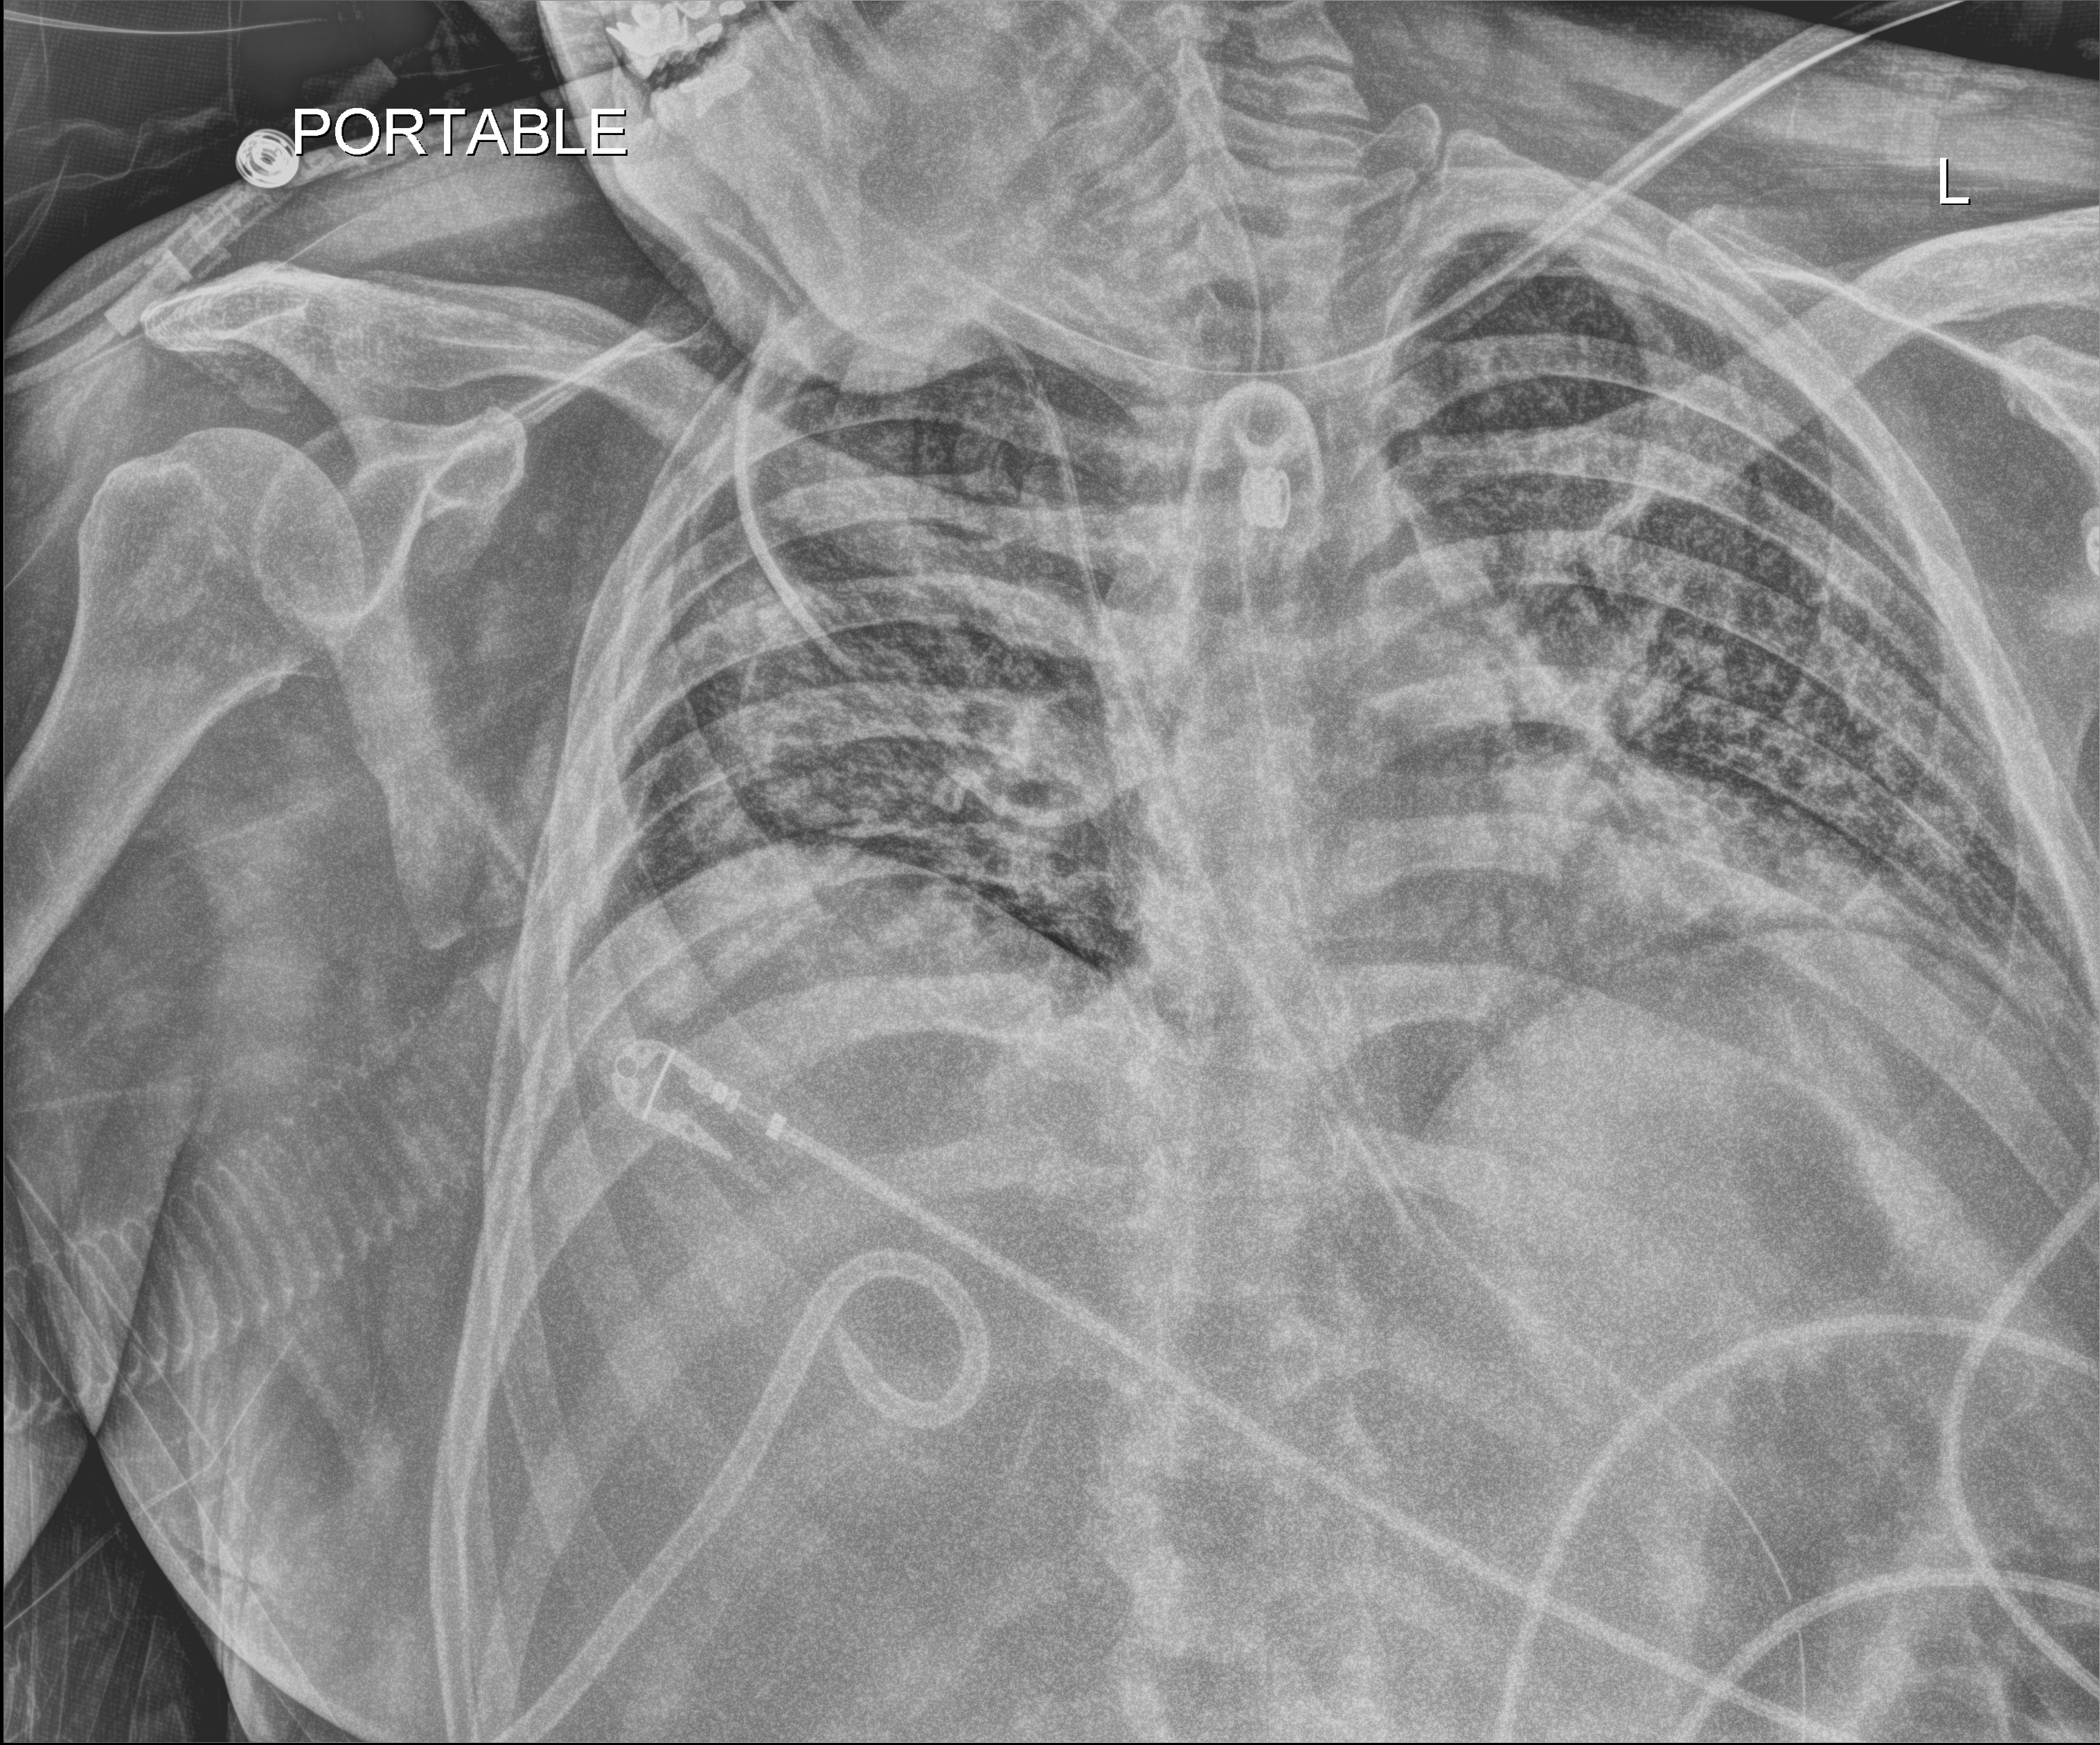
Bedside chest radiograph (digital radiography). Male patient hospitalised with COVID-19, age 18–59 years.
Admission-level facts for this patient (not findings on this image; timing relative to this image not recorded): hypertension (admission record): yes.